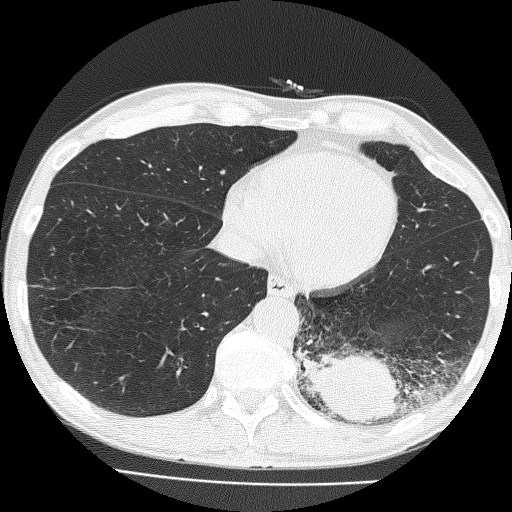
Chest CT (low-dose screening protocol), one axial image; baseline annual screen; lung window (W 1500 / L -600 HU); 2 mm slice thickness; 120 kVp; slice 109 of 160 in the series; 512 × 512 image matrix. Male, age 58 years at enrolment. Current smoker at enrolment.
- Expert reader's lesion annotation, bounding box [x1, y1, x2, y2] px = [290, 294, 430, 435].
- The screening reader recorded 2 non-calcified nodules or masses ≥4 mm on this exam; which of them this box marks is not recorded.